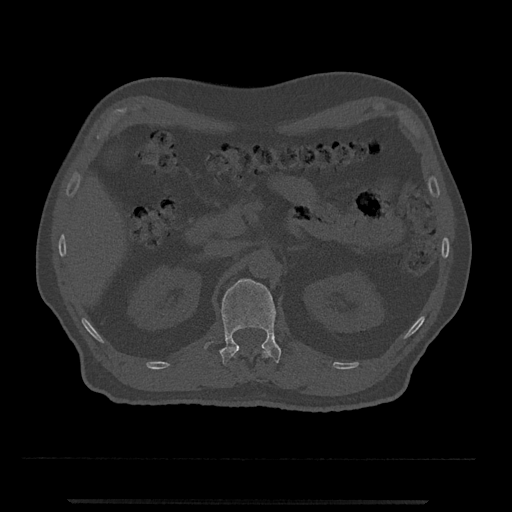
CT including the spine, one axial slice; slice 353 of 797 in the series (ordered by position); reconstruction kernel Br40s/3; 120 kVp; bone window (W 1800 / L 400 HU); 0.5 mm slice thickness; 512 × 512 image matrix, field of view 419 × 419 mm. Patient: male, 63 years. Case-level facts recorded for this patient, not image findings: primary cancer: prostate.
Outlined on this slice (semi-automatically segmented with operator editing):
- L1 vertebra: box from (x=204, y=278) to (x=281, y=365) px
- T12 vertebra: (x=233, y=348)–(x=270, y=358)